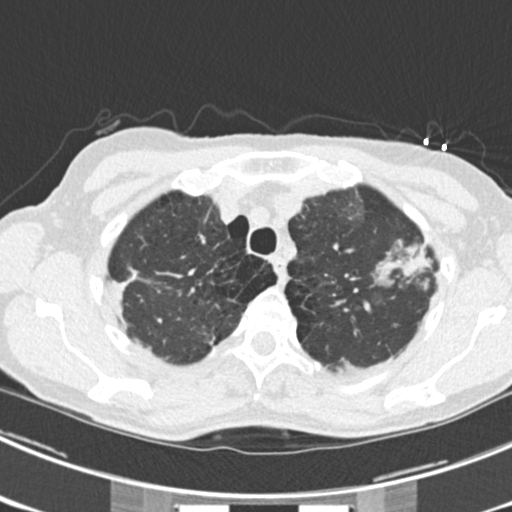
Chest CT (low-dose screening protocol), one axial image. Third screening round (two years after baseline). Lung window (W 1500 / L -600 HU). 2 mm slice thickness. 120 kVp. 512 × 512 image matrix. Female, age 63 years at enrolment. Current smoker at enrolment.
• Lesion marked by an expert reader, bounding box (x1, y1, x2, y2) in pixels: (375, 232, 444, 294).
• The screening reader recorded 9 non-calcified nodules or masses ≥4 mm on this exam (left upper lobe, right upper lobe, left upper lobe, left lower lobe, right middle lobe, left lower lobe, left lower lobe, right lower lobe, right lower lobe); which of them this box marks is not recorded.
• Lung cancer was diagnosed 15 days after this screen: bronchiolo-alveolar adenocarcinoma, NOS, right upper lobe, right middle lobe, right lower lobe, left upper lobe, left lower lobe, moderately differentiated (G2), stage IV (AJCC 6th edition).